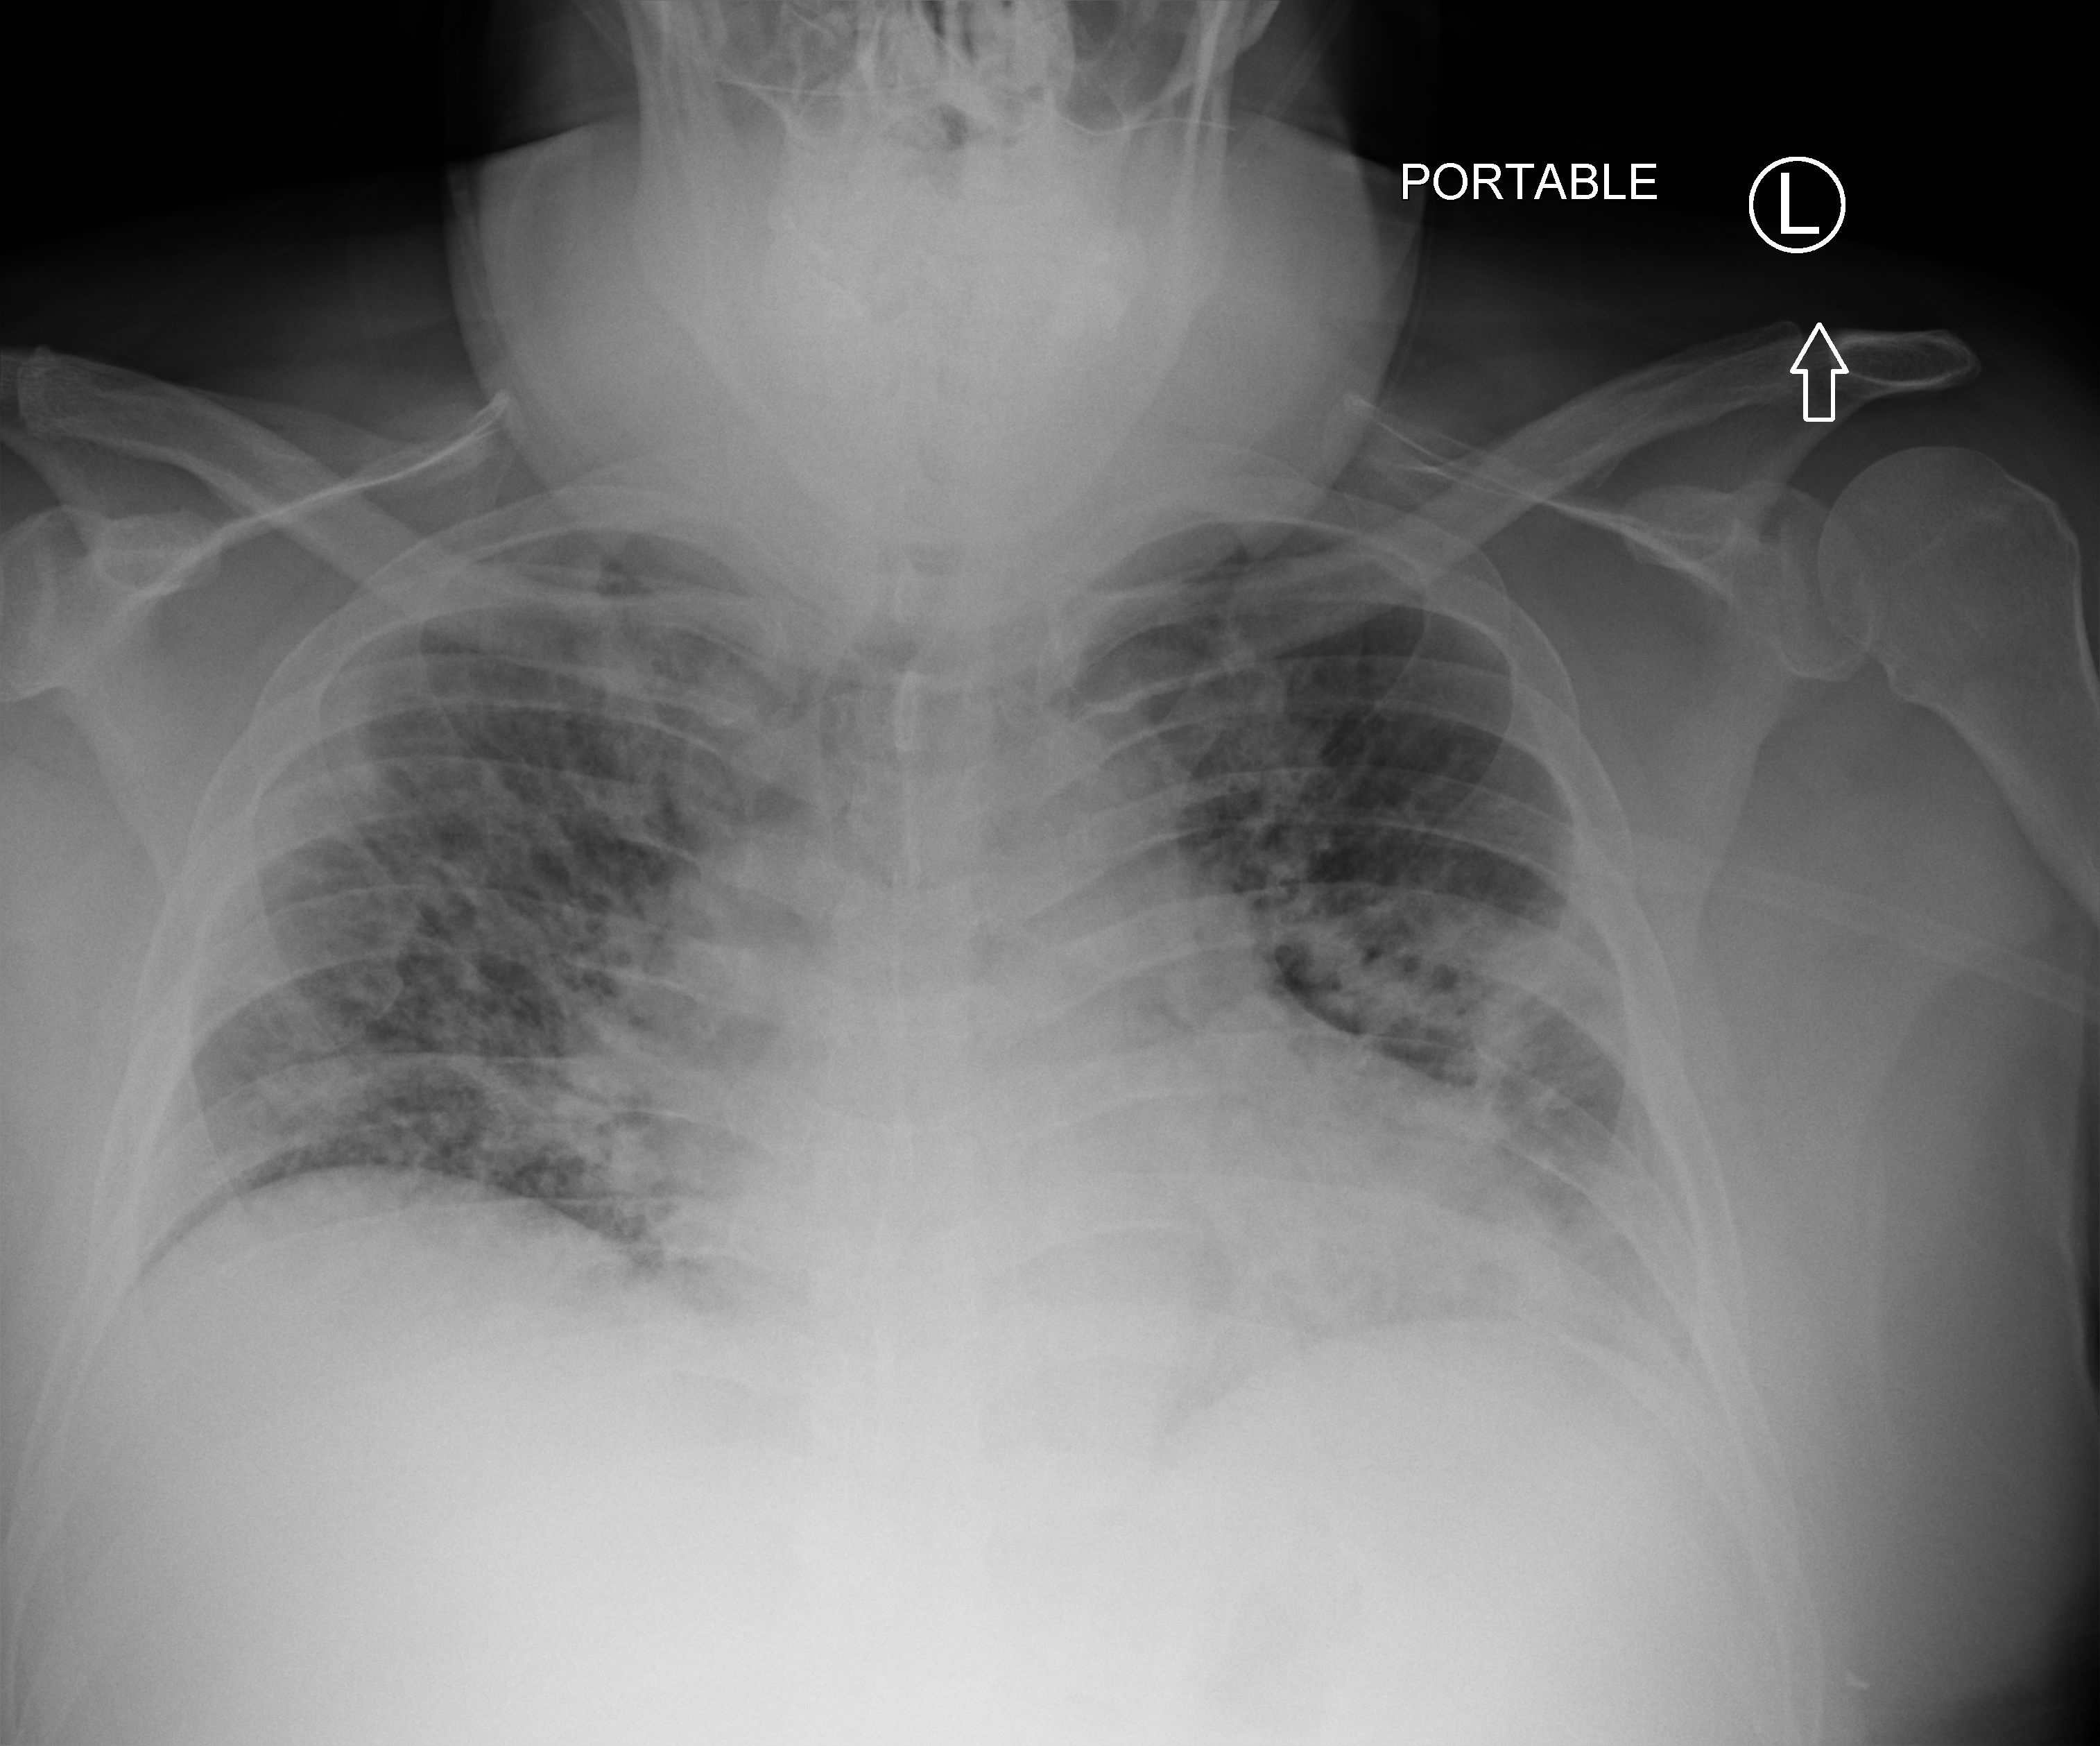
Bedside chest radiograph (computed radiography), anteroposterior (AP) projection. Male patient hospitalised with COVID-19, age 18–59 years.
Hospital-stay facts (about this admission, not read from this image; timing relative to this image not recorded): admitted to intensive care during this hospital stay: no; mechanically ventilated during this hospital stay: no.